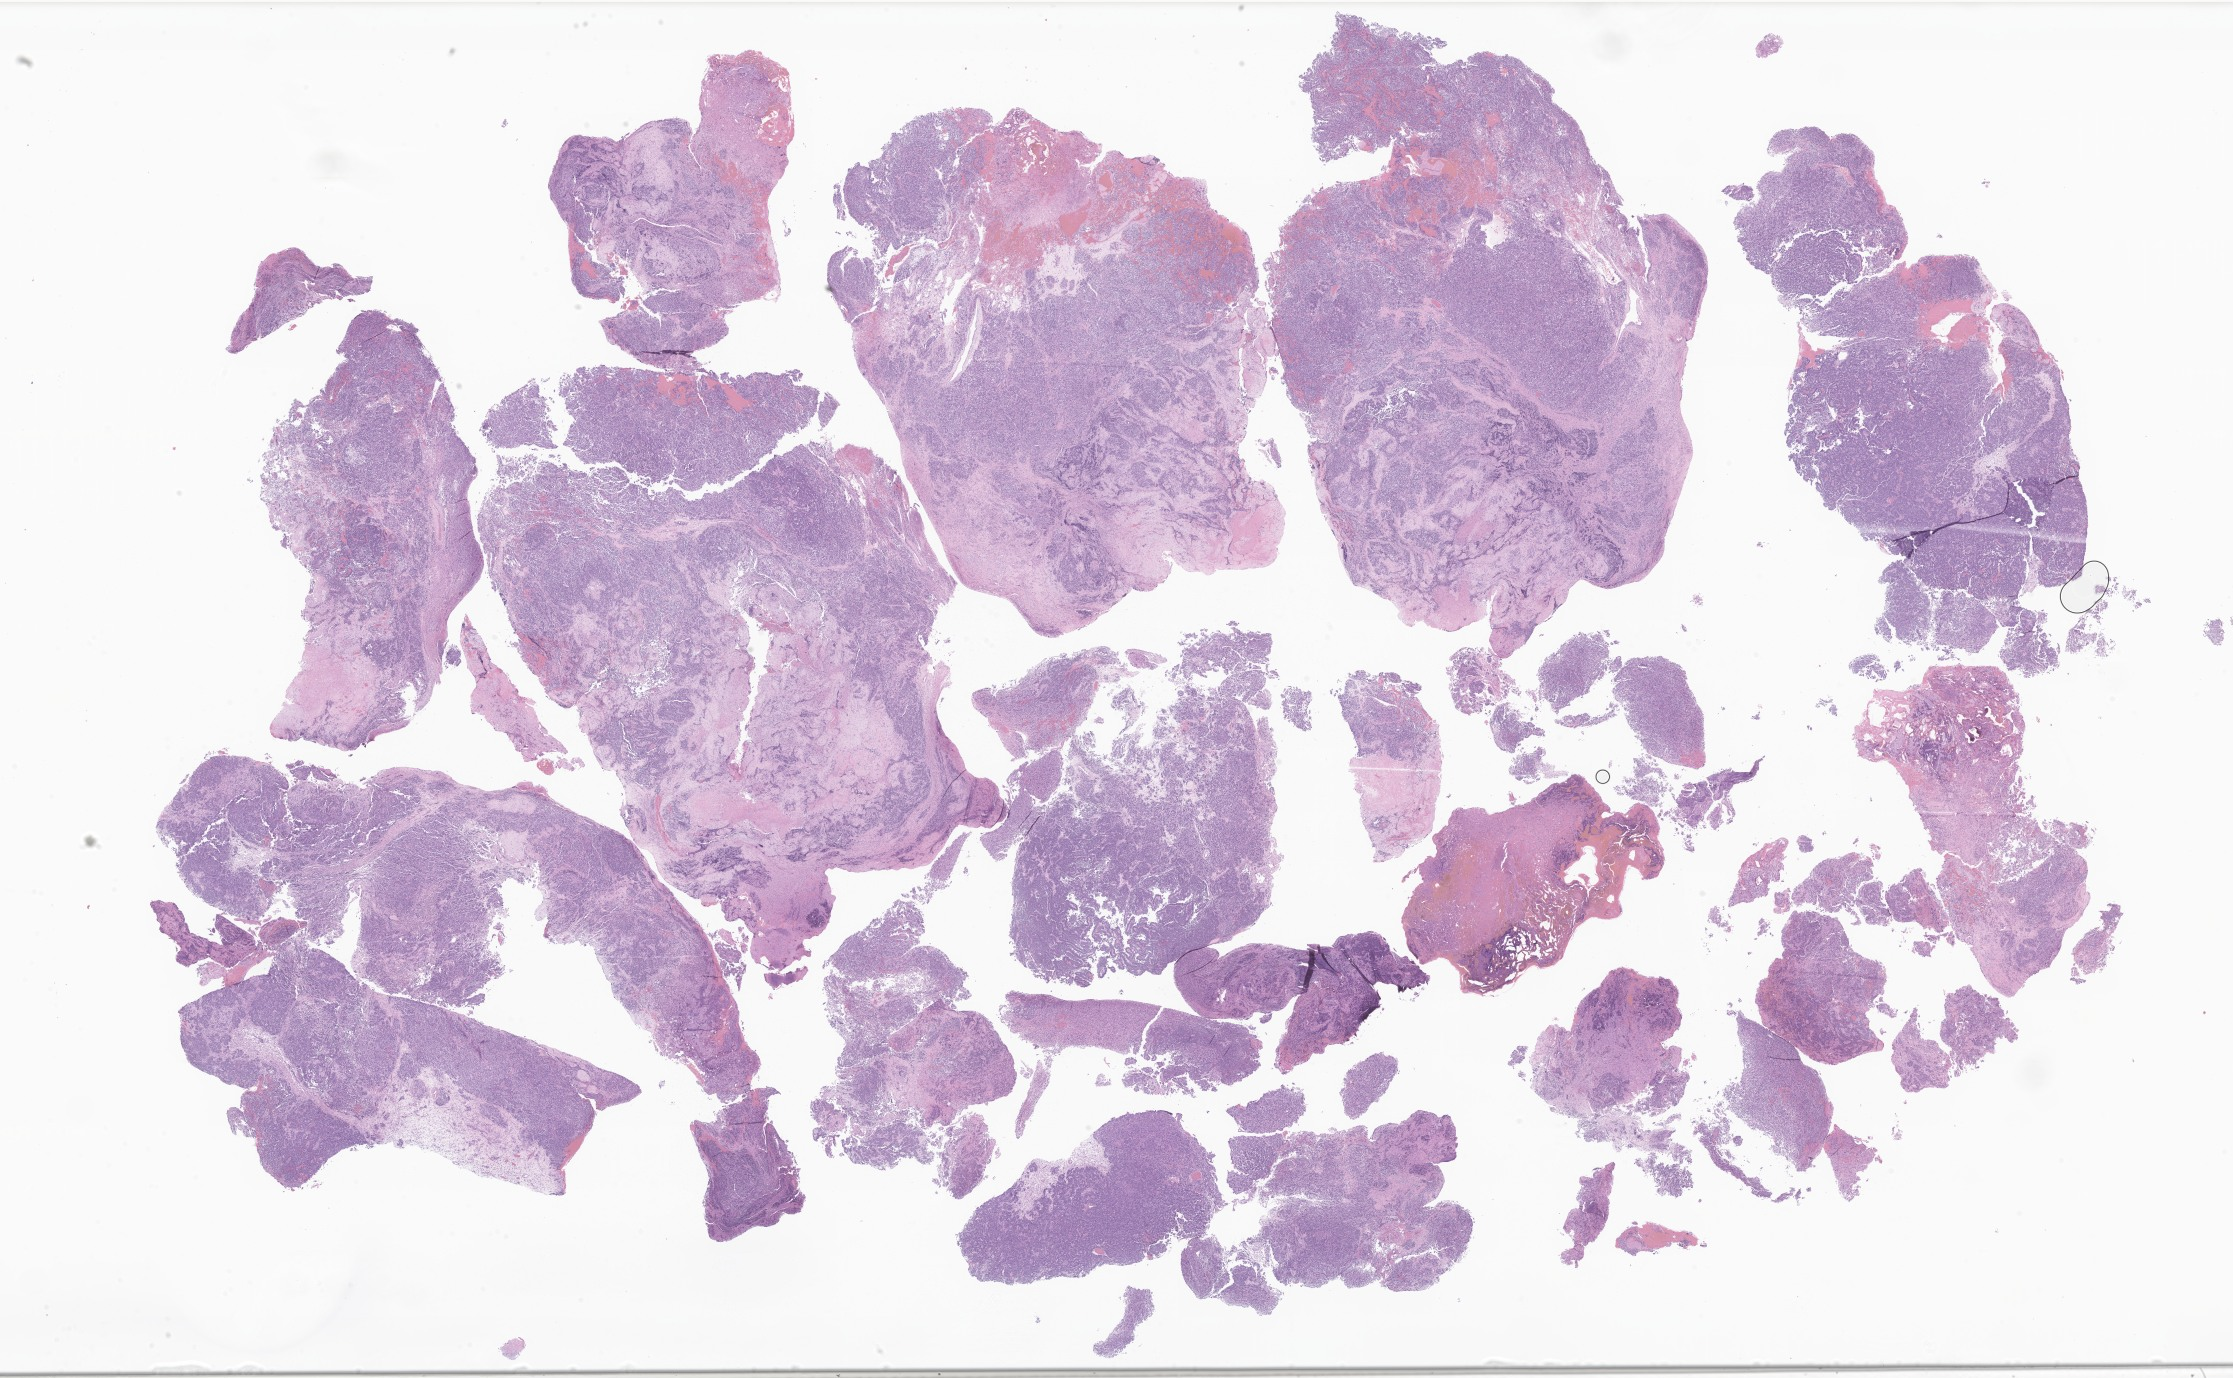
Whole-slide image, hematoxylin and eosin (H&E) stain of tumor tissue from the brain — a low-resolution overview of the entire scanned area, about 37.7 x 23.2 mm; formalin-fixed, paraffin-embedded (FFPE) tissue. Patient: male, age 47 months (3 years 11 months).
Recorded diagnosis: CNS embryonal tumor, NOS.